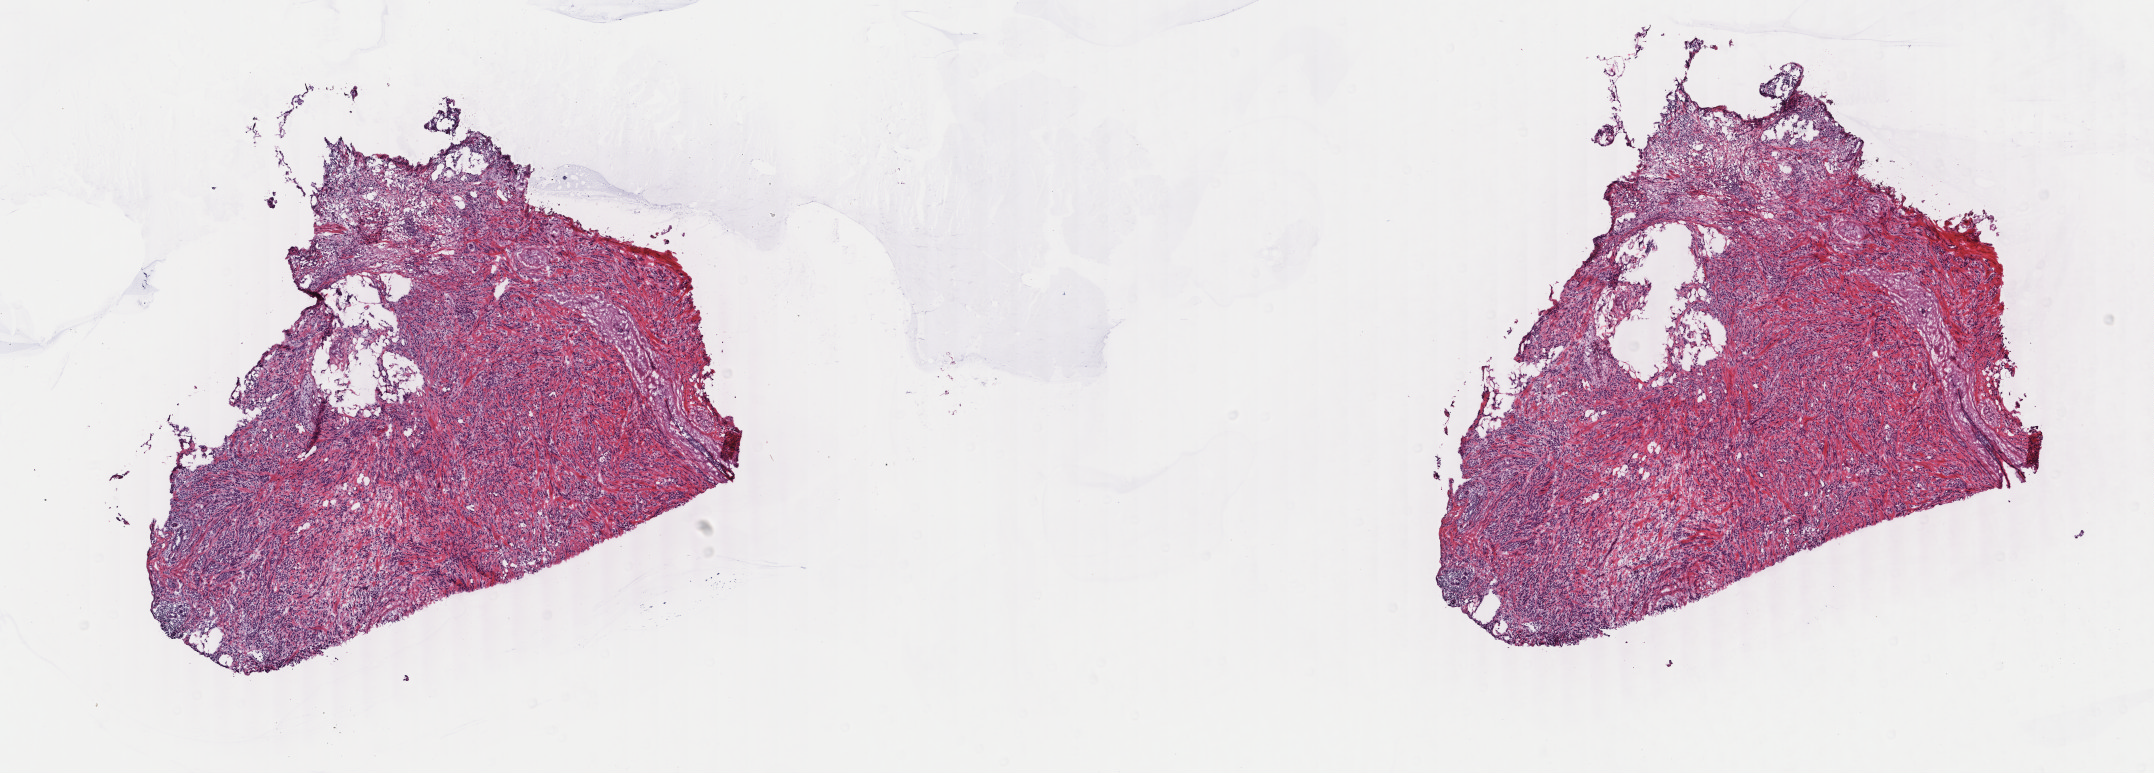
H&E whole-slide image — a low-resolution overview of the entire scanned area, about 17.1 x 6.1 mm (slide scanned at 40x). Frozen section from the top of the tissue portion. Breast, primary tumour sample. Patient: female, age at initial diagnosis 70 years. Composition of this section per pathologist review: tumour cells 85%, tumour nuclei 85%, normal cells 2%, stromal cells 13%, necrosis 0%. Inflammatory infiltration, as recorded: lymphocyte infiltration 1%, monocyte infiltration 0%, neutrophil infiltration 0%.
AJCC pathologic stage: IIA. TNM: T2 N0 (i+) M0. Histologic diagnosis: Lobular carcinoma, NOS. Lymph nodes positive (case pathology): 0 of 4 examined.